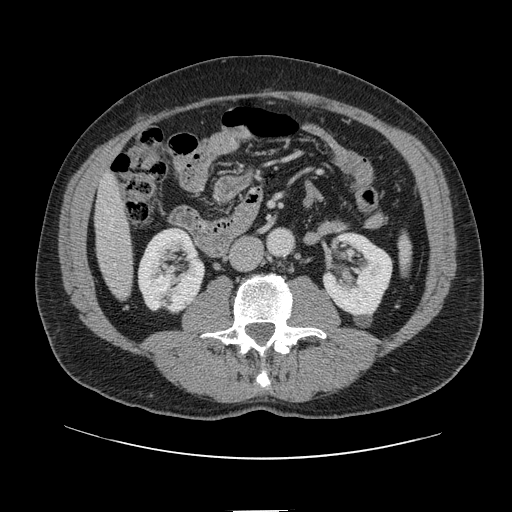
Contrast-enhanced abdominal CT, one axial slice; slice 20 of 161 in the series (ordered by position); intravenous contrast given; soft-tissue window (W 400 / L 40 HU); 2.5 mm slice thickness; 512 × 512 image matrix, field of view 412 × 412 mm. Male patient, age 66 years. Case-level facts recorded for this patient, not image findings: diagnosis: colorectal cancer liver metastases, imaged before liver resection.
Annotated regions visible in this slice (manually delineated by an expert):
- liver: bounding box [x1, y1, x2, y2] px = [96, 178, 131, 298]
- planned liver remnant (the part of the liver to remain after resection): [95, 178, 127, 252]